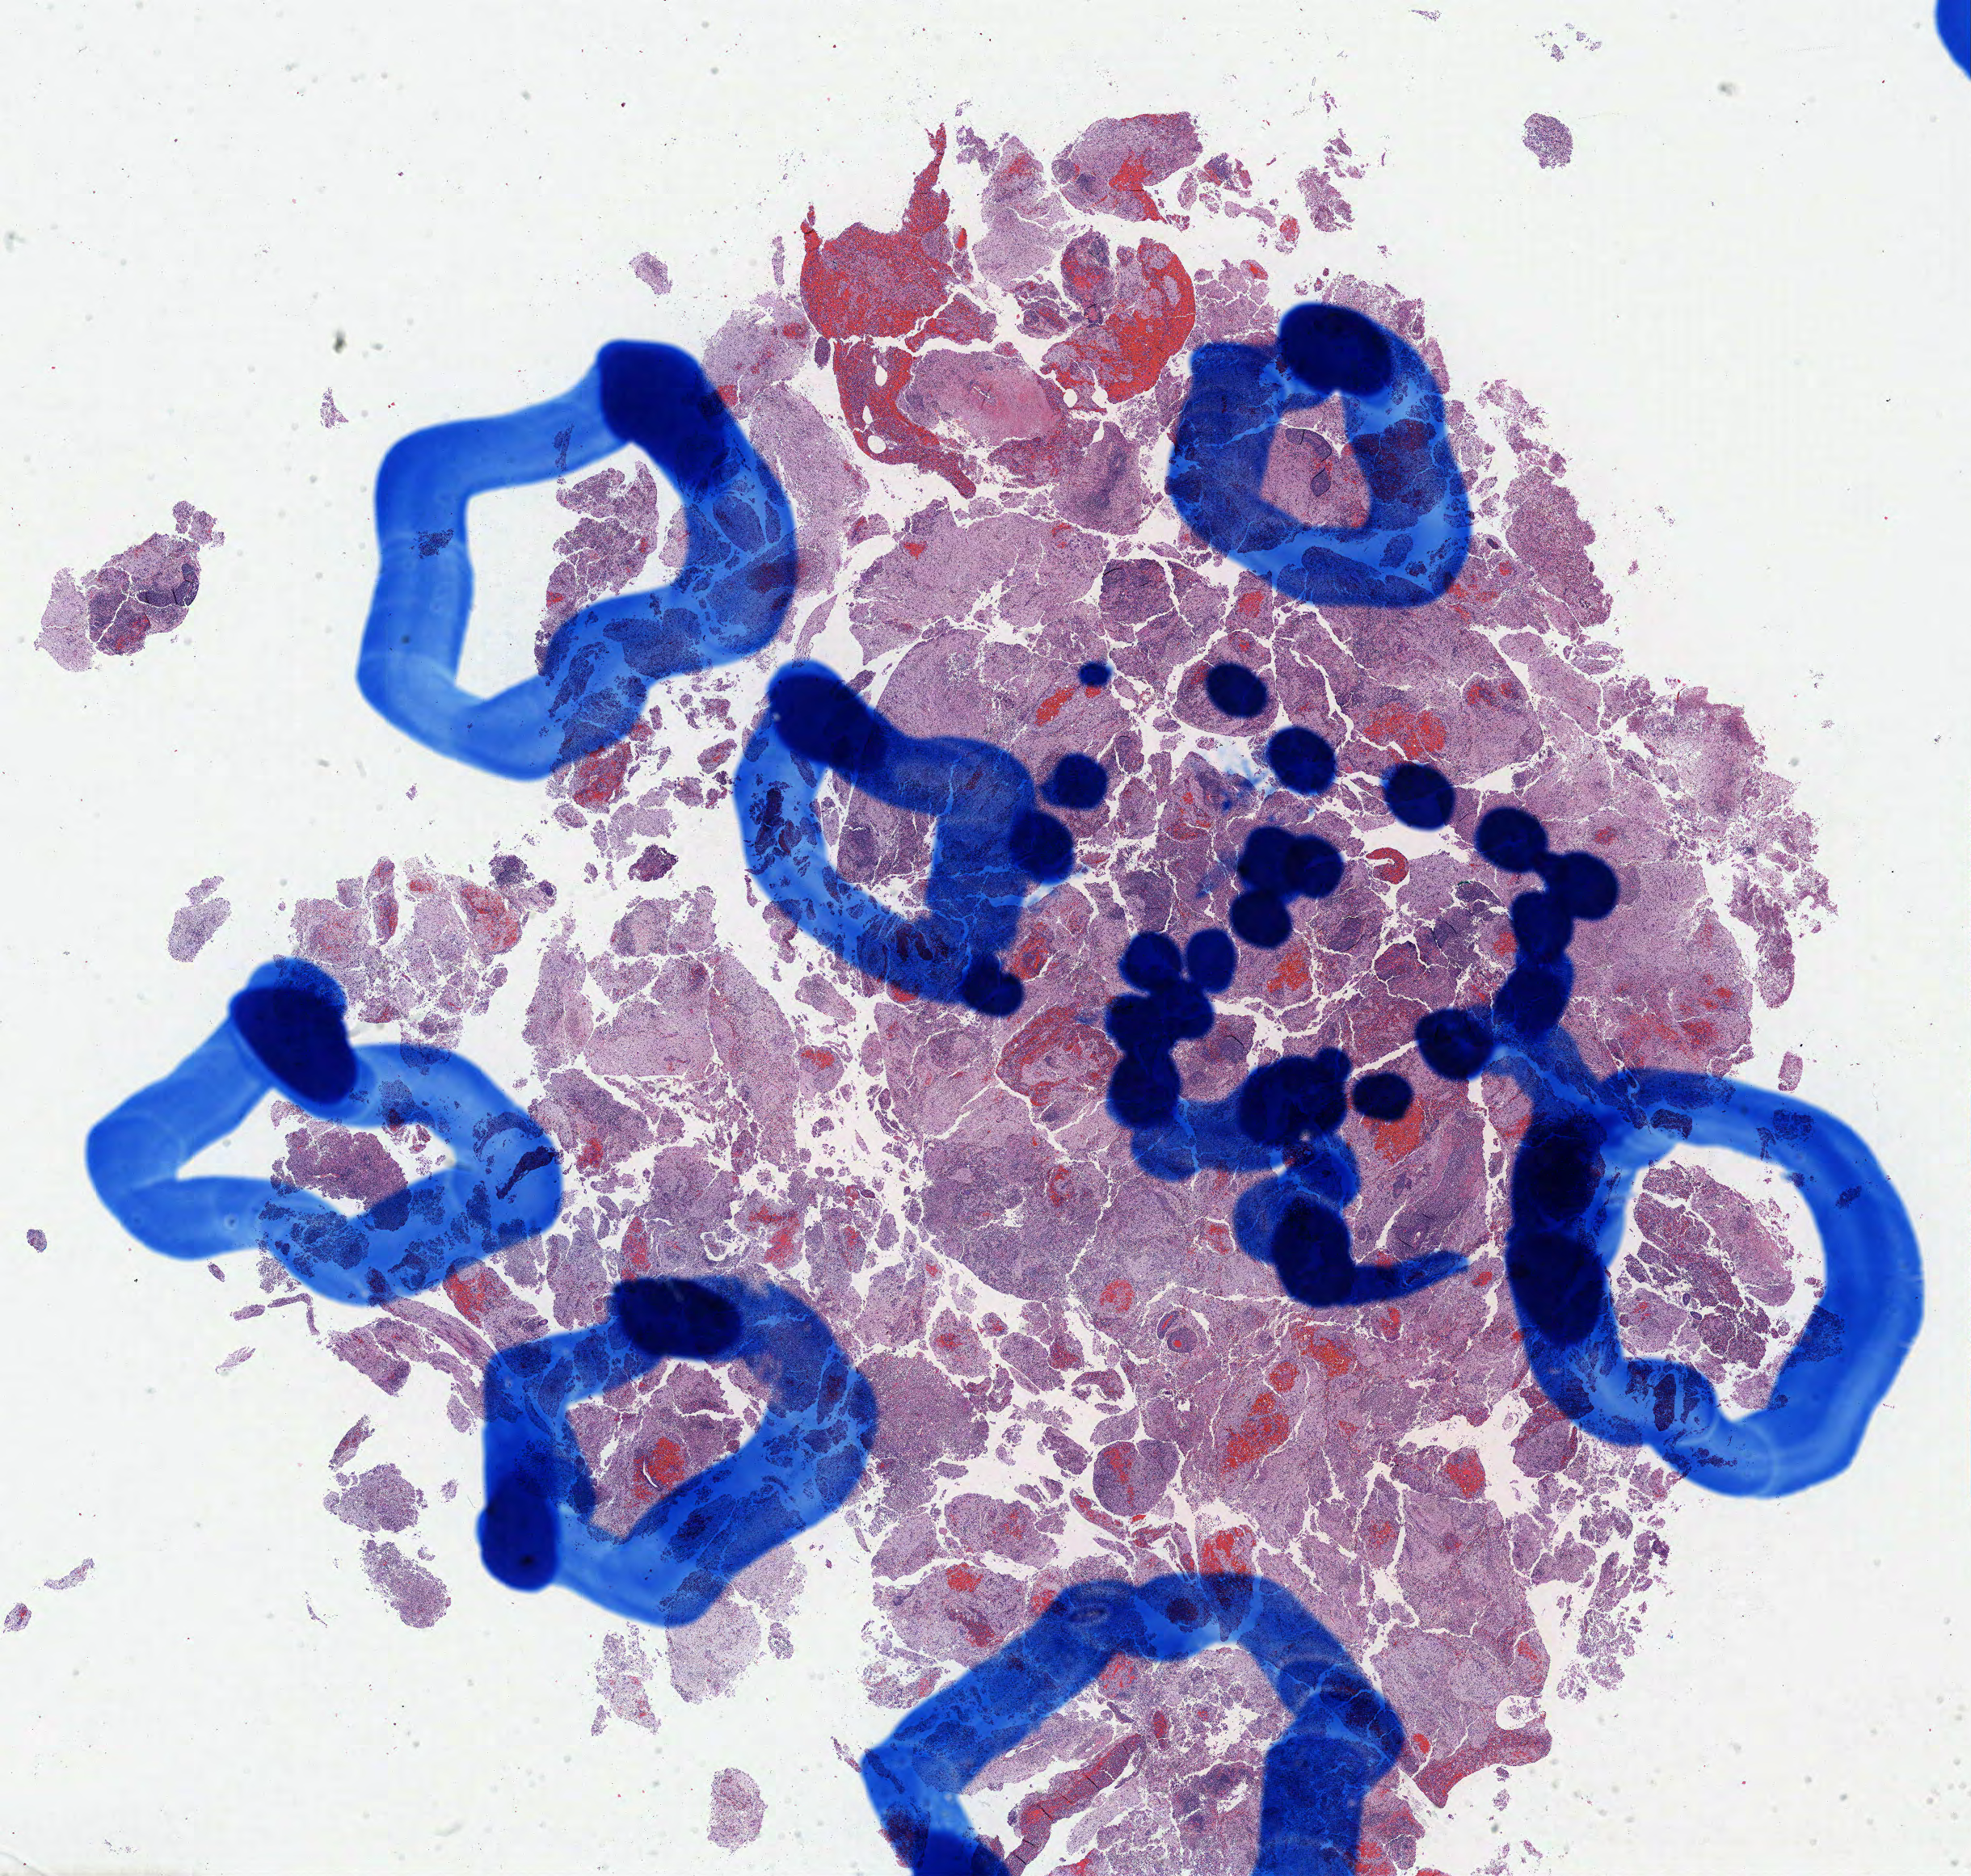
Whole-slide image, hematoxylin and eosin (H&E) stain, shown as a low-resolution overview of the whole scanned area (about 19.2 x 18.3 mm). Tumor tissue. Site: brain. Male patient, 51 years old.
Diagnosis: Diffuse large B-cell lymphoma, NOS.